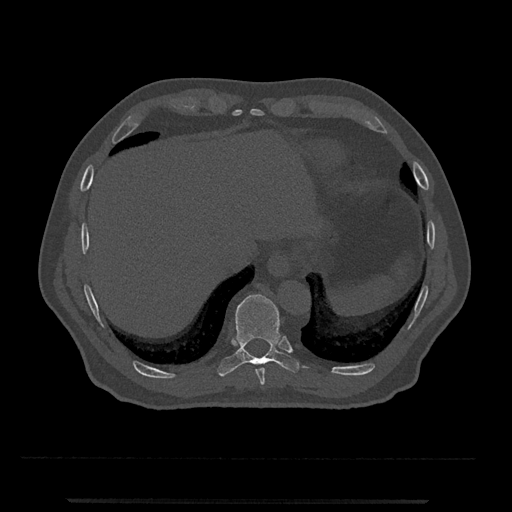
CT including the spine, one axial slice; slice 531 of 797 in the series (ordered by position); reconstruction kernel Br40s/3; bone window (W 1800 / L 400 HU); 0.5 mm slice thickness; 512 × 512 image matrix. Patient: male, 63 years. Case-level facts recorded for this patient, not image findings: primary cancer: prostate.
Structures marked on this image (semi-automatic segmentation, software-assisted and operator-edited):
- T10 vertebra: bounding box (x1, y1, x2, y2) in pixels: (217, 294, 301, 377)
- T9 vertebra: (256, 368, 265, 385)